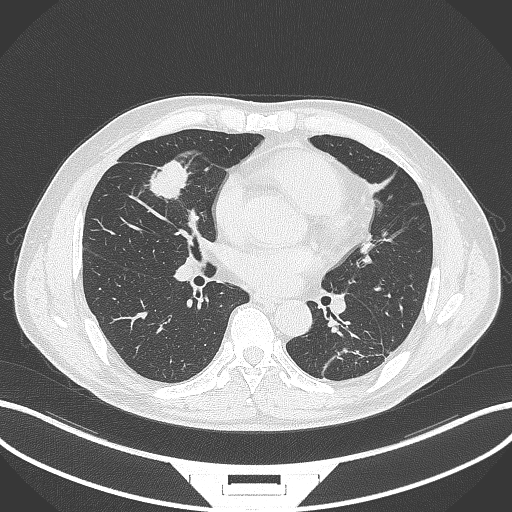
Chest CT, one axial slice. Slice 141 of 399 in the series (ordered by position). Reconstruction kernel B70f. 120 kVp. Lung window (W 1500 / L -600 HU). 1 mm slice thickness. 512 × 512 image matrix, field of view 400 × 400 mm. Patient: male, 59 years. From the clinical record (not read from this slice): clinical TNM (as recorded): T2a N1 M0.
Outlined on this slice (bounding box drawn by a radiologist):
- lung tumour (recorded histology: adenocarcinoma): bounding box [x1, y1, x2, y2] px = [150, 158, 194, 203]